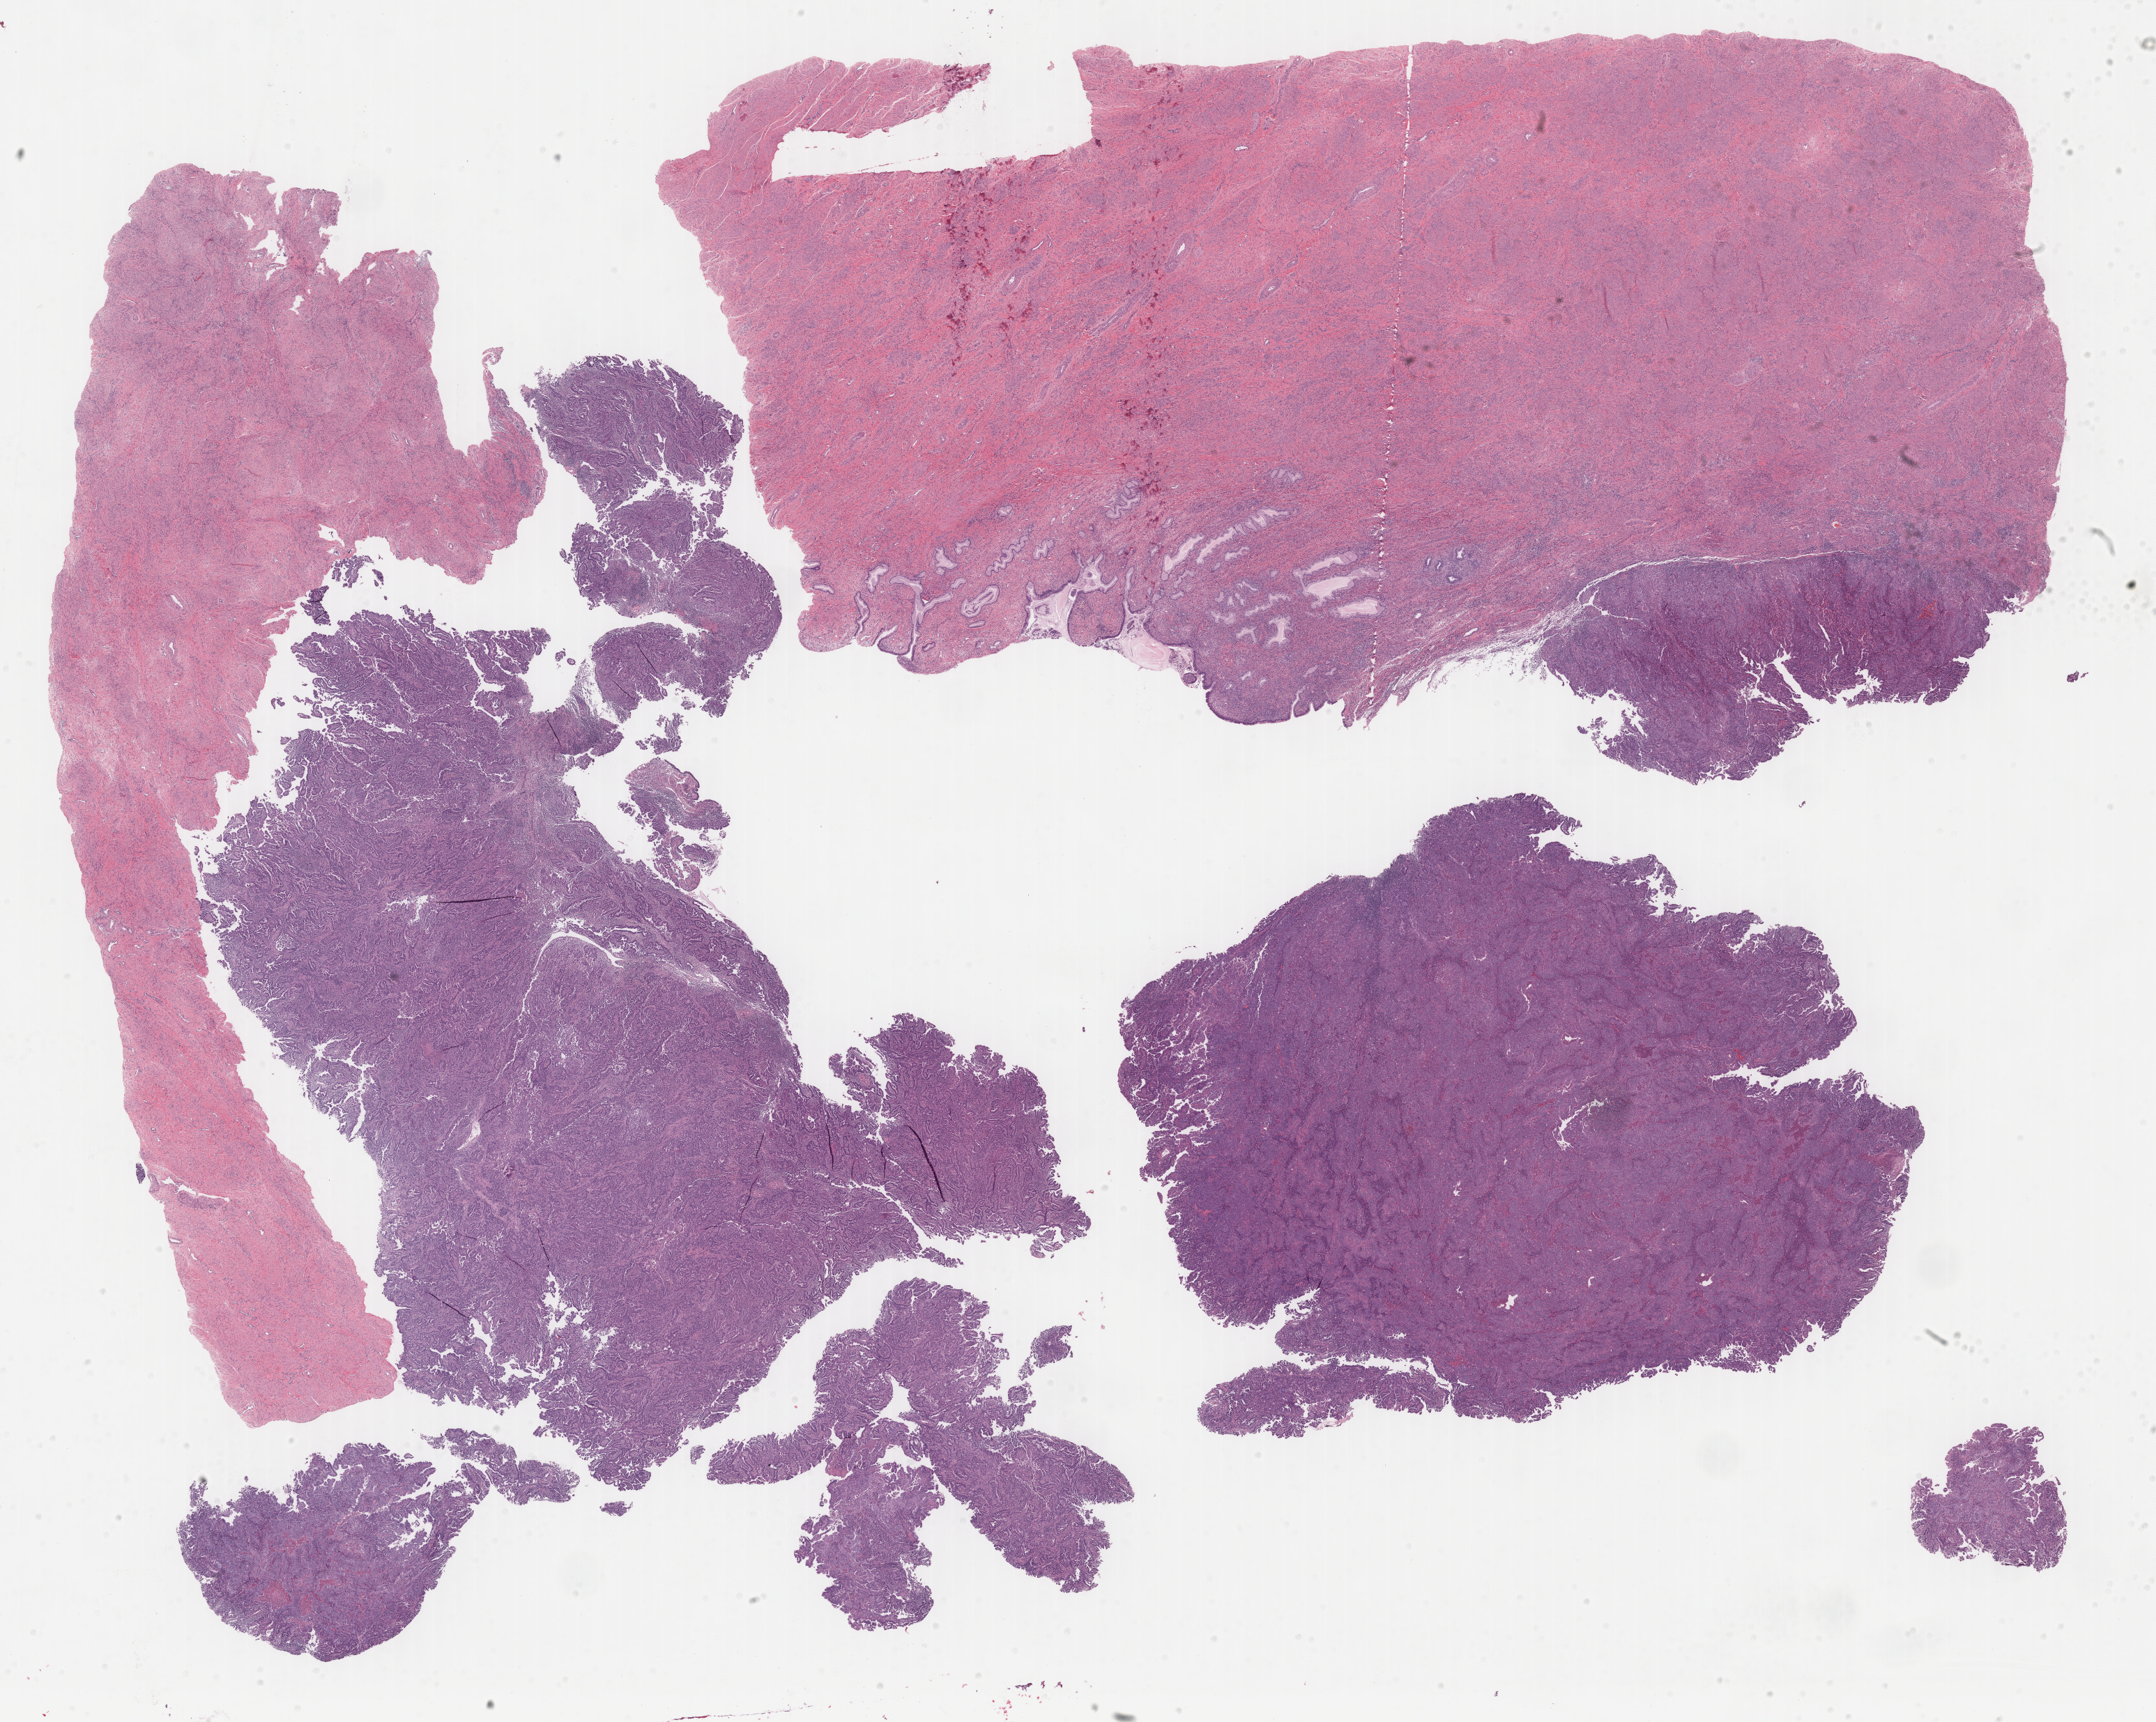
Digitized Hematoxylin and eosin (H&E) stained tissue section (whole slide) — low-resolution overview of the scanned area, about 24.6 x 19.6 mm, formalin-fixed paraffin-embedded (FFPE) diagnostic section, primary tumour sample from the uterus. Patient: female, age at initial diagnosis 45 years.
Diagnosis: Serous cystadenocarcinoma, NOS (endometrium).